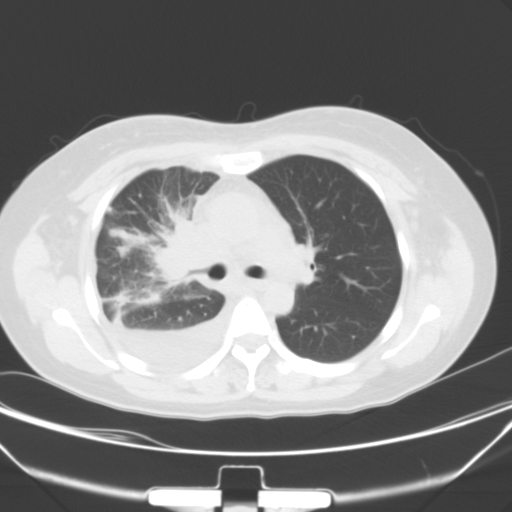
Chest CT, one axial slice. Position 22 of 40 along the scan axis. 120 kVp. Lung window (W 1500 / L -600 HU). 512 × 512 image matrix, field of view 352 × 352 mm. Patient: female, 36 years. Case-level facts recorded for this patient, not image findings: clinical TNM (as recorded): T1b N2 M0.
Structures marked on this image (rectangle marked by the reading radiologist):
- lung tumour (recorded histology: adenocarcinoma): bounding box (x1, y1, x2, y2) in pixels: (151, 209, 204, 286)